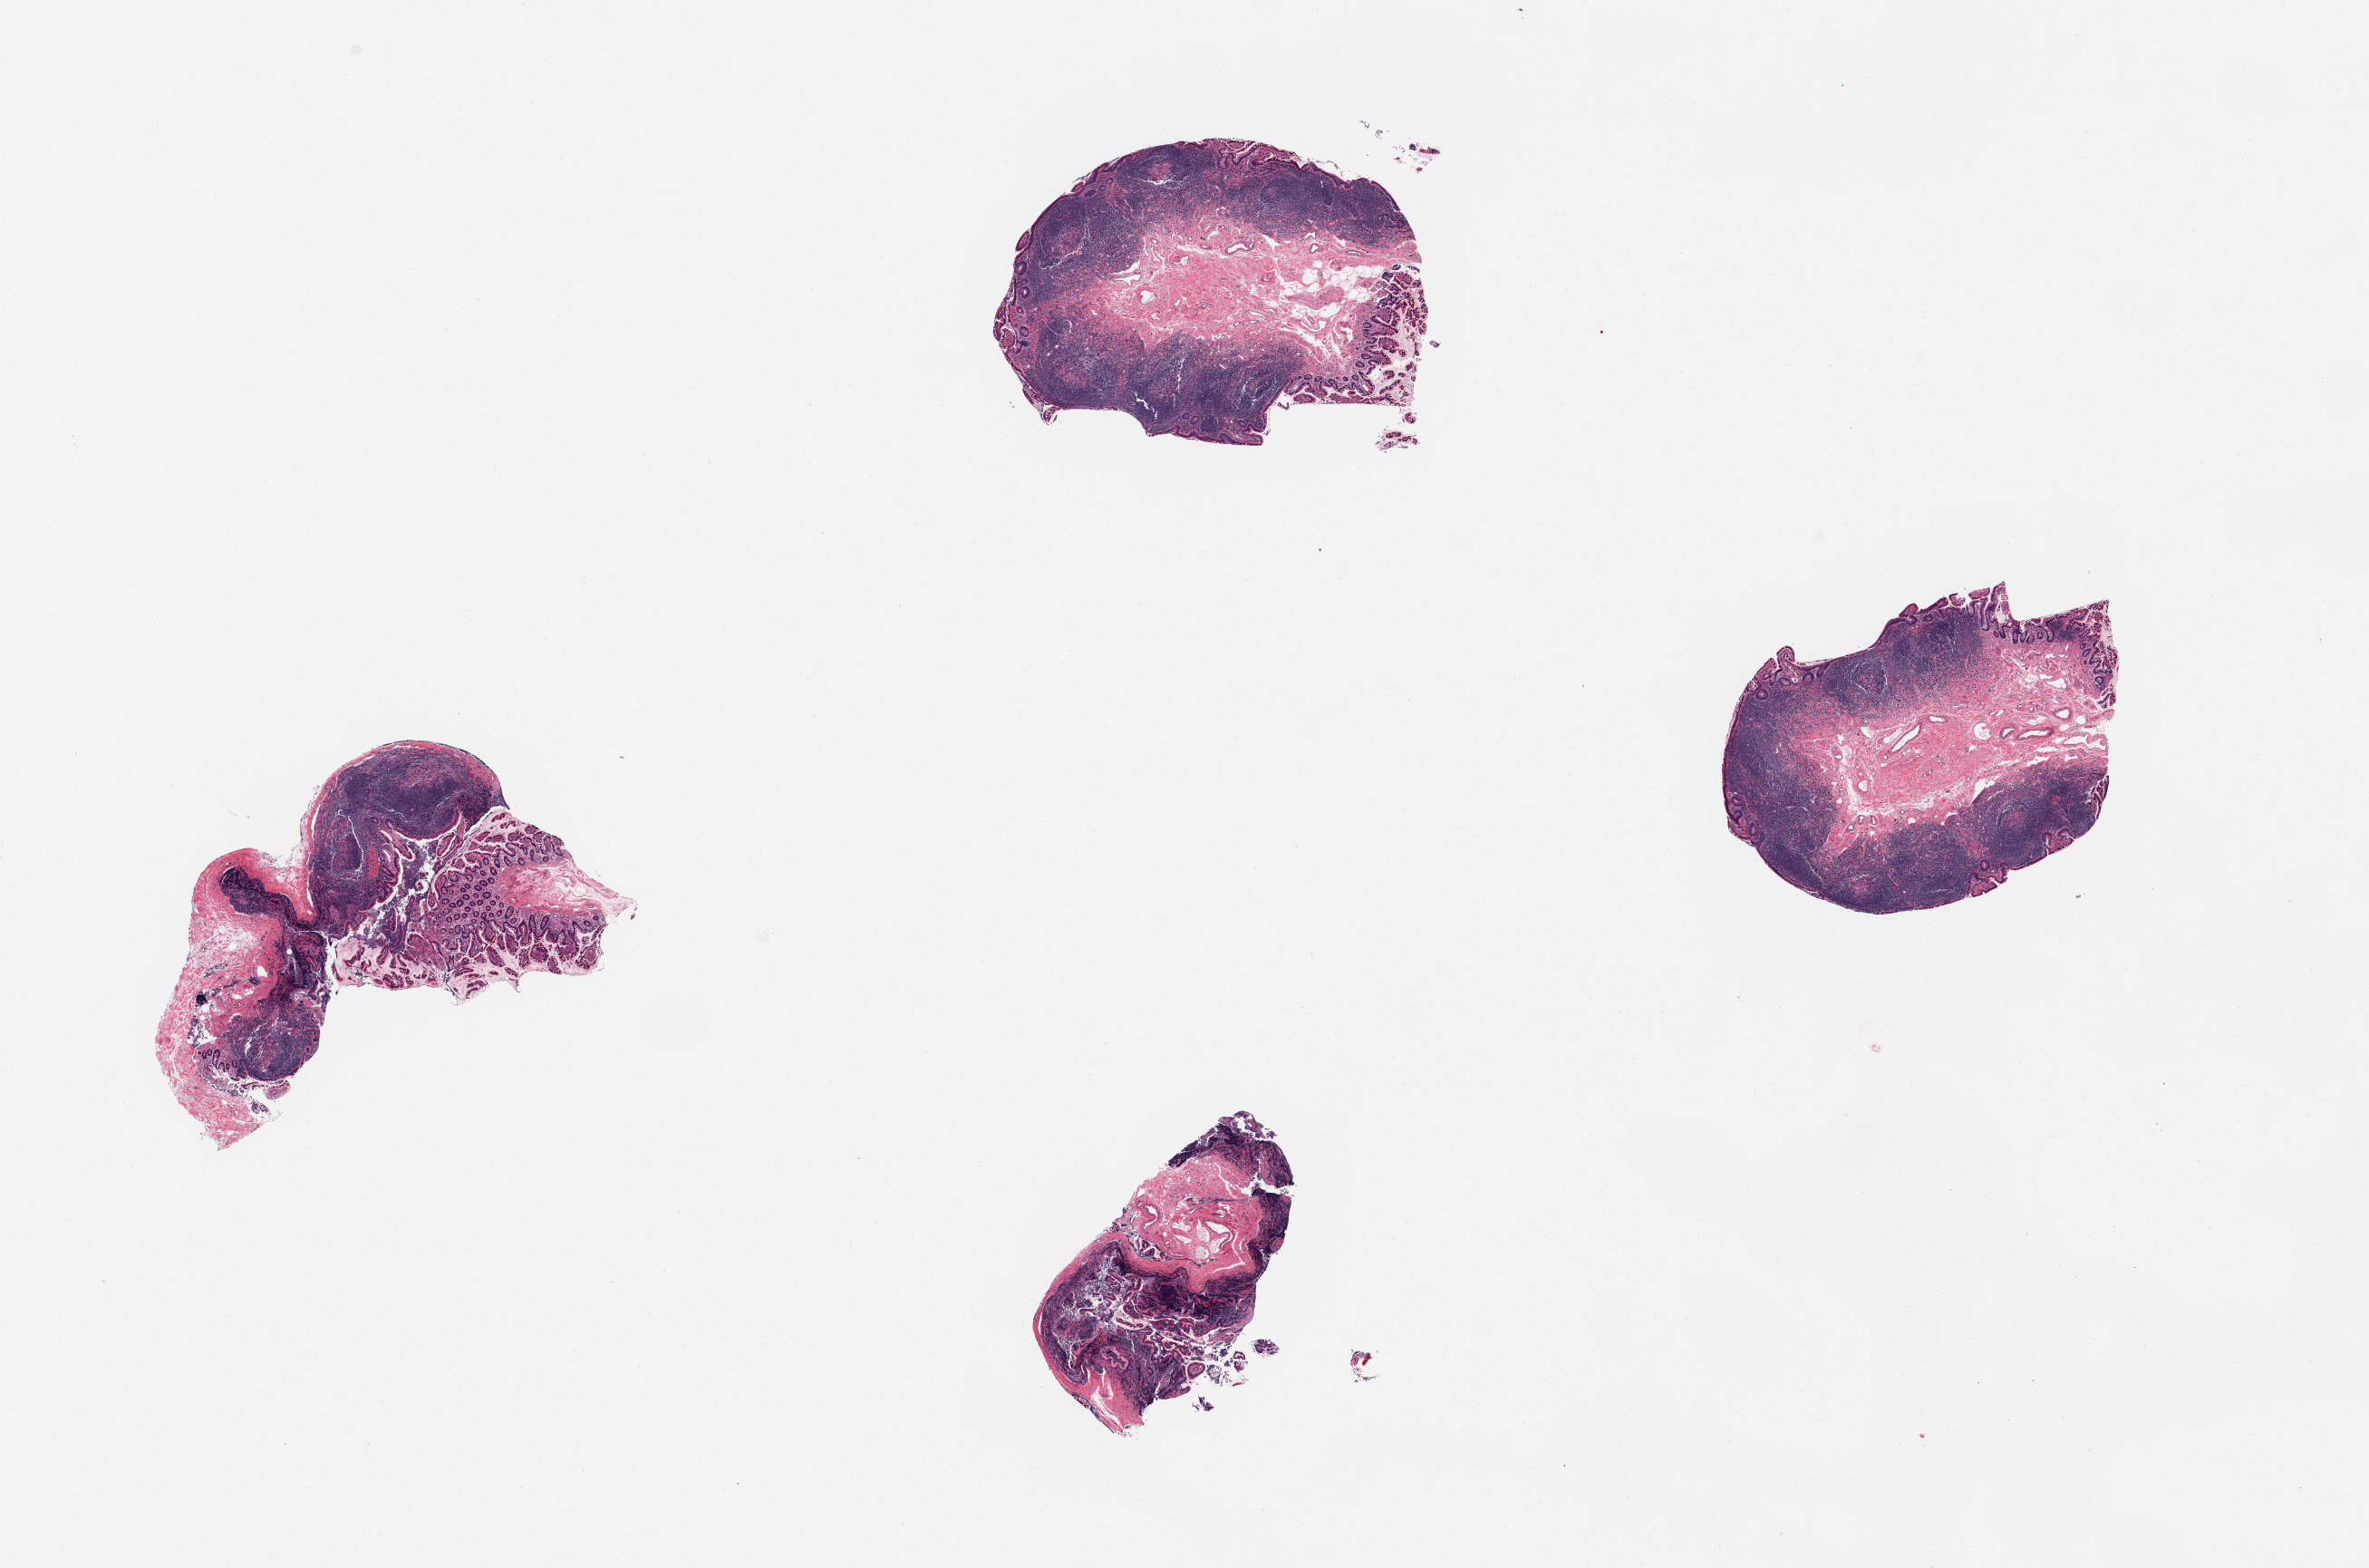
Whole-slide image, H&E stain — low-resolution overview of the scanned area, about 20.7 x 13.7 mm (acquisition: 20x scan). PAXgene-fixed, paraffin-embedded tissue. Section of ileum (target tissue). Donor tissue sample. Male donor.
Review note (as recorded): 4 pieces; abundant mucosal lymphoid tissue well dissected.